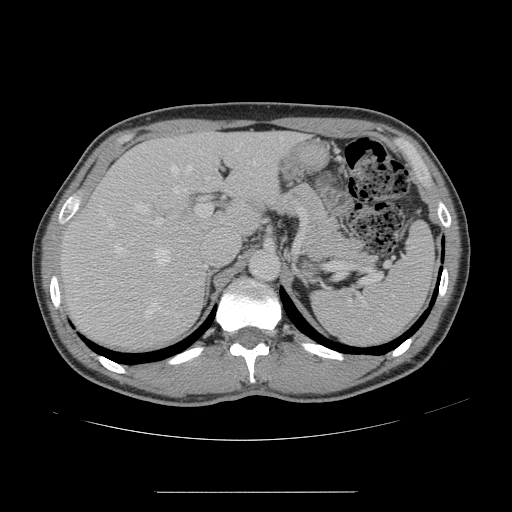
Contrast-enhanced abdominal CT, one axial slice. Slice 101 of 178 in the series (ordered by position). Intravenous contrast given. Soft-tissue window (W 400 / L 40 HU). 2.5 mm slice thickness. 512 × 512 image matrix, field of view 401 × 401 mm. Male patient, age 53 years. Case-level facts recorded for this patient, not image findings: diagnosis: colorectal cancer liver metastases, imaged before liver resection; multiple liver metastases: yes; largest metastasis: 2.4 cm; disease in both lobes: no.
Outlined on this slice (manually delineated by an expert):
- hepatic veins: box from (x=112, y=147) to (x=256, y=317) px
- liver: (x=62, y=134)–(x=301, y=348)
- planned liver remnant (the part of the liver to remain after resection): (x=148, y=134)–(x=299, y=231)
- portal vein (with intrahepatic branches): (x=133, y=202)–(x=212, y=227)